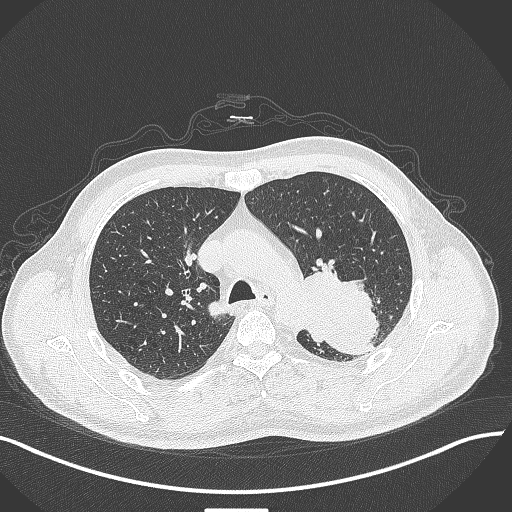
Chest CT, one axial slice; position 300 of 429 along the scan axis; lung window (W 1500 / L -600 HU); 512 × 512 image matrix, field of view 400 × 400 mm. Male patient, age 55 years. From the clinical record (not read from this slice): clinical TNM (as recorded): T3 N0 M1c.
Outlined on this slice (rectangle marked by the reading radiologist):
- lung tumour (recorded histology: adenocarcinoma): bounding box <298,265,380,361> (left, top, right, bottom; pixels)